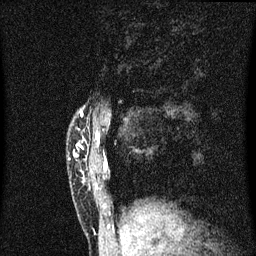
Breast MRI (dynamic contrast-enhanced), one sagittal slice. Slice 10 of 60 in the series (ordered by position). Dynamic contrast-enhanced series, image 2 of 3 at this slice position (ordered by acquisition). 1.5 T. TE 4.2 ms, TR 8.4 ms. 2 mm slice thickness. 256 × 256 image matrix, field of view 200 × 200 mm. Patient: female, 40 years.
Outlined on this slice (semi-automatic segmentation, software-assisted and operator-edited):
- analysis volume of interest (the breast-tissue region the enhancement analysis was run in; not a lesion): bounding box (x1, y1, x2, y2) in pixels: (70, 110, 102, 203)
- tumour enhancement mask (voxels above the 70 % enhancement threshold inside the analysis volume of interest): (82, 112, 84, 115)